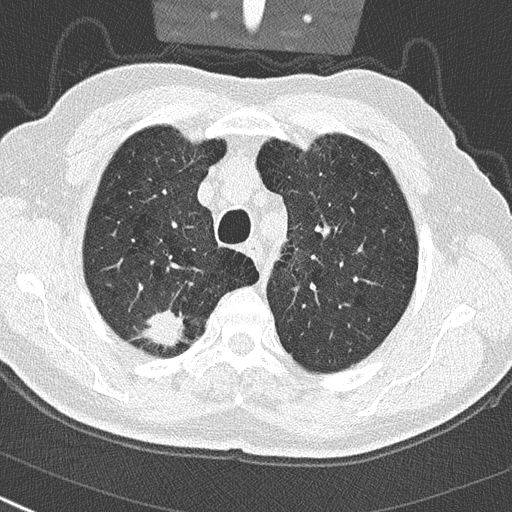
Axial slice from a low-dose chest CT screening exam. First (baseline) screen. Lung window (W 1500 / L -600 HU). 2 mm slice thickness. 512 × 512 image matrix, field of view 300 × 300 mm. Male participant, aged 65 years at enrolment. Current smoker at enrolment.
Expert-annotated lung lesion, bounding box (x1, y1, x2, y2) in pixels: (133, 302, 189, 355). Reader record for this screening exam (exam-level; its link to the box is not recorded): non-calcified nodule or mass ≥4 mm, right upper lobe, 24 × 19 mm, spiculated (stellate) margins, soft tissue attenuation. Official screen result: positive, change unspecified: nodule(s) >= 4 mm or enlarging nodule(s), mass(es), or other non-specific abnormalities suspicious for lung cancer.